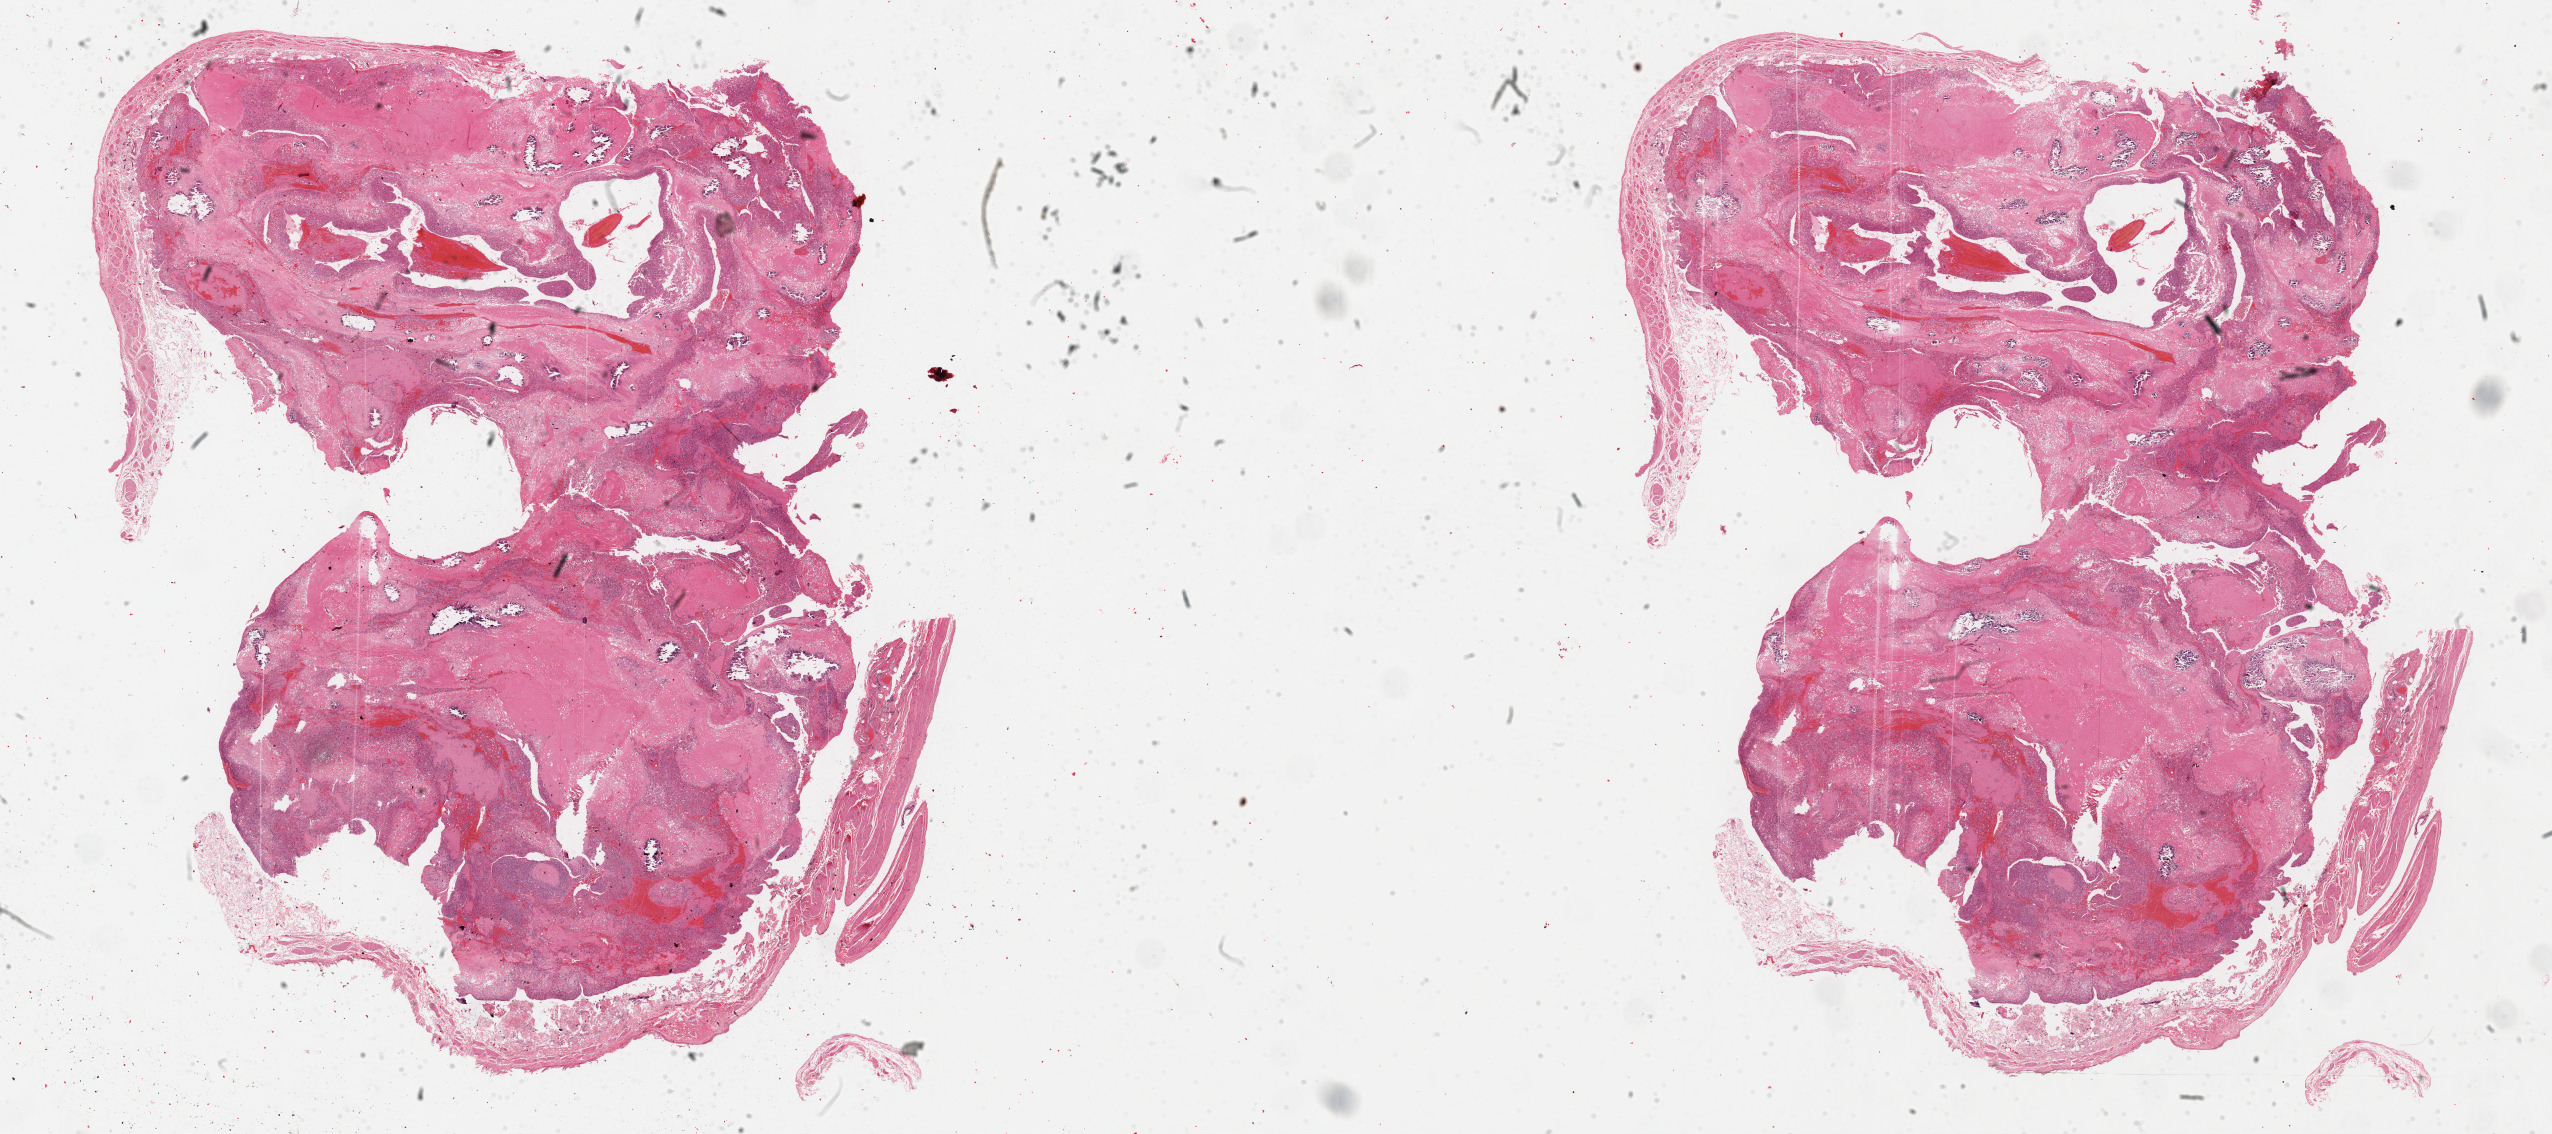
Digitized Hematoxylin and eosin (H&E) stained tissue section (whole slide), low-resolution overview of the scanned area, about 41.3 x 18.3 mm (slide scanned at 40x), formalin-fixed paraffin-embedded (FFPE) diagnostic section, adrenal cortex, primary tumour sample. Male patient; age at initial diagnosis 49 years.
Histologic diagnosis: Adrenal cortical carcinoma. Laterality: left.